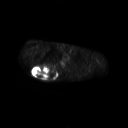
FDG PET of an extremity soft-tissue mass (from a PET/CT study), one axial slice; position 193 of 267 along the scan axis; 128 × 128 image matrix. Male patient, age 61 years. From the clinical record (not read from this slice): histological type: pleiomorphic spindle cell undifferentiated; grade: high; site of the primary tumour: right parascapusular.
Annotated regions visible in this slice (expert contour drawn on MRI and transferred to this co-registered scan by the dataset authors):
- gross tumour volume including surrounding oedema: box from (x=32, y=64) to (x=60, y=79) px
- gross tumour volume (mass): (x=32, y=64)–(x=57, y=78)